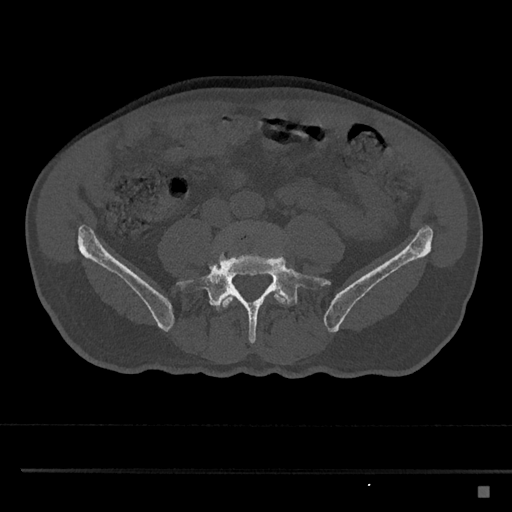
CT including the spine, one axial slice; position 597 of 797 along the scan axis; reconstruction kernel Br40s/3; 120 kVp; bone window (W 1800 / L 400 HU); 0.5 mm slice thickness; 512 × 512 image matrix, field of view 391 × 391 mm. Male patient, age 59 years. Case-level facts recorded for this patient, not image findings: primary cancer: prostate.
Structures marked on this image (semi-automatically segmented with operator editing):
- L4 vertebra: bounding box <216,225,289,311> (left, top, right, bottom; pixels)
- L5 vertebra: <176,244,330,344>